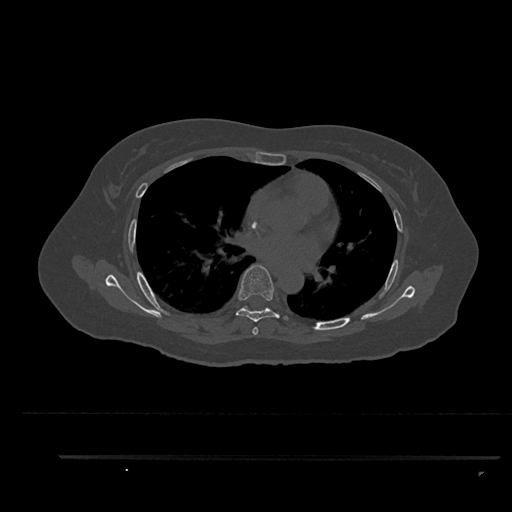
CT including the spine, one axial slice. Slice 557 of 797 in the series (ordered by position). Reconstruction kernel Br40s/3. 120 kVp. Bone window (W 1800 / L 400 HU). 0.5 mm slice thickness. 512 × 512 image matrix. Female patient, age 44 years. Case-level facts recorded for this patient, not image findings: primary cancer: renal; vertebrae with lytic lesions (as recorded): L1.
Structures marked on this image (semi-automatically segmented with operator editing):
- T5 vertebra: box from (x=253, y=327) to (x=258, y=334) px
- T6 vertebra: (x=235, y=264)–(x=288, y=335)